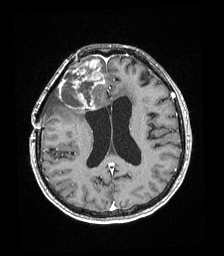
Brain MRI from a brain-tumour surgery series, one axial slice. Position 85 of 192 along the scan axis. T1-weighted post-contrast. 1 mm slice thickness. 224 × 256 image matrix, field of view 219 × 250 mm. Case-level facts recorded for this patient, not image findings: histopathology: Astrocytoma; WHO grade: 4; IDH mutation: yes; tumour location: Right superficial frontal.
Outlined on this slice (manually delineated by an expert):
- tumour: box from (x=59, y=60) to (x=105, y=109) px